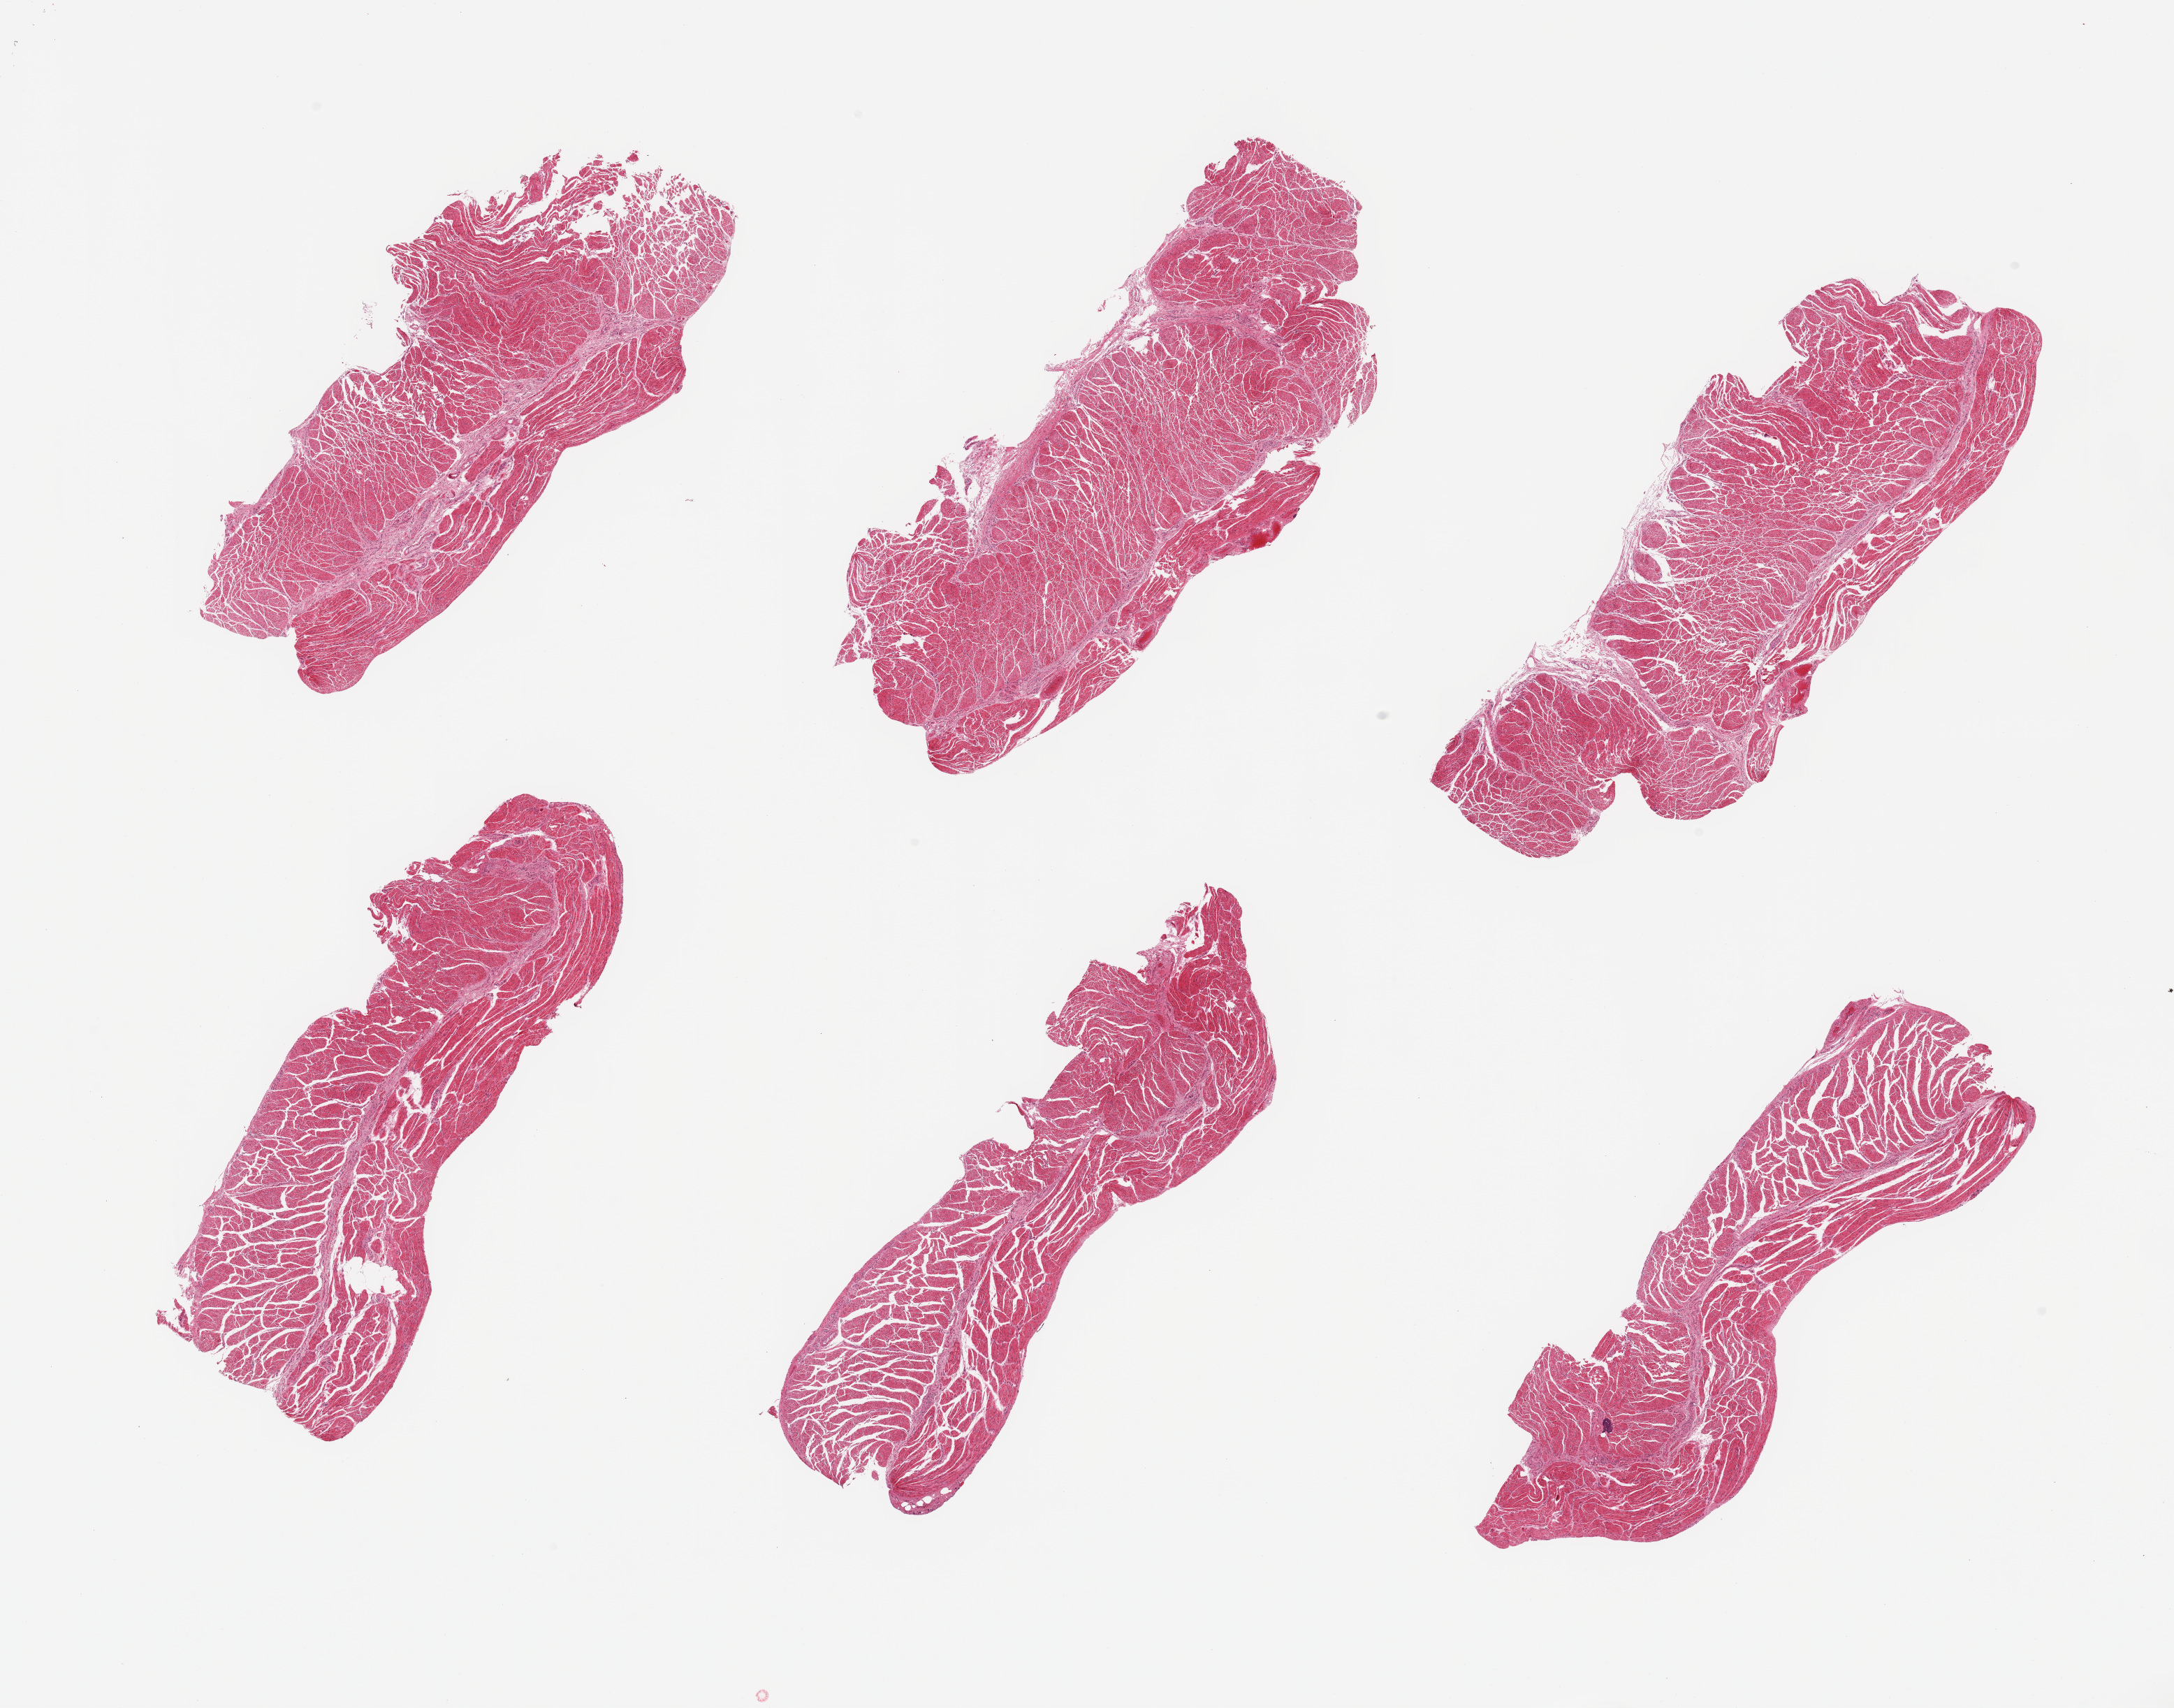
Whole-slide image, haematoxylin and eosin stain, a low-resolution overview of the entire scanned area, about 24.6 x 19.3 mm (slide scanned at 20x). PAXgene-fixed paraffin-embedded (PFPE) section. Target tissue: esophageal muscle. Tissue donor sample. Donor sex: female.
* pathologist's review note for this sample: 6 pieces, confirmed muscularis